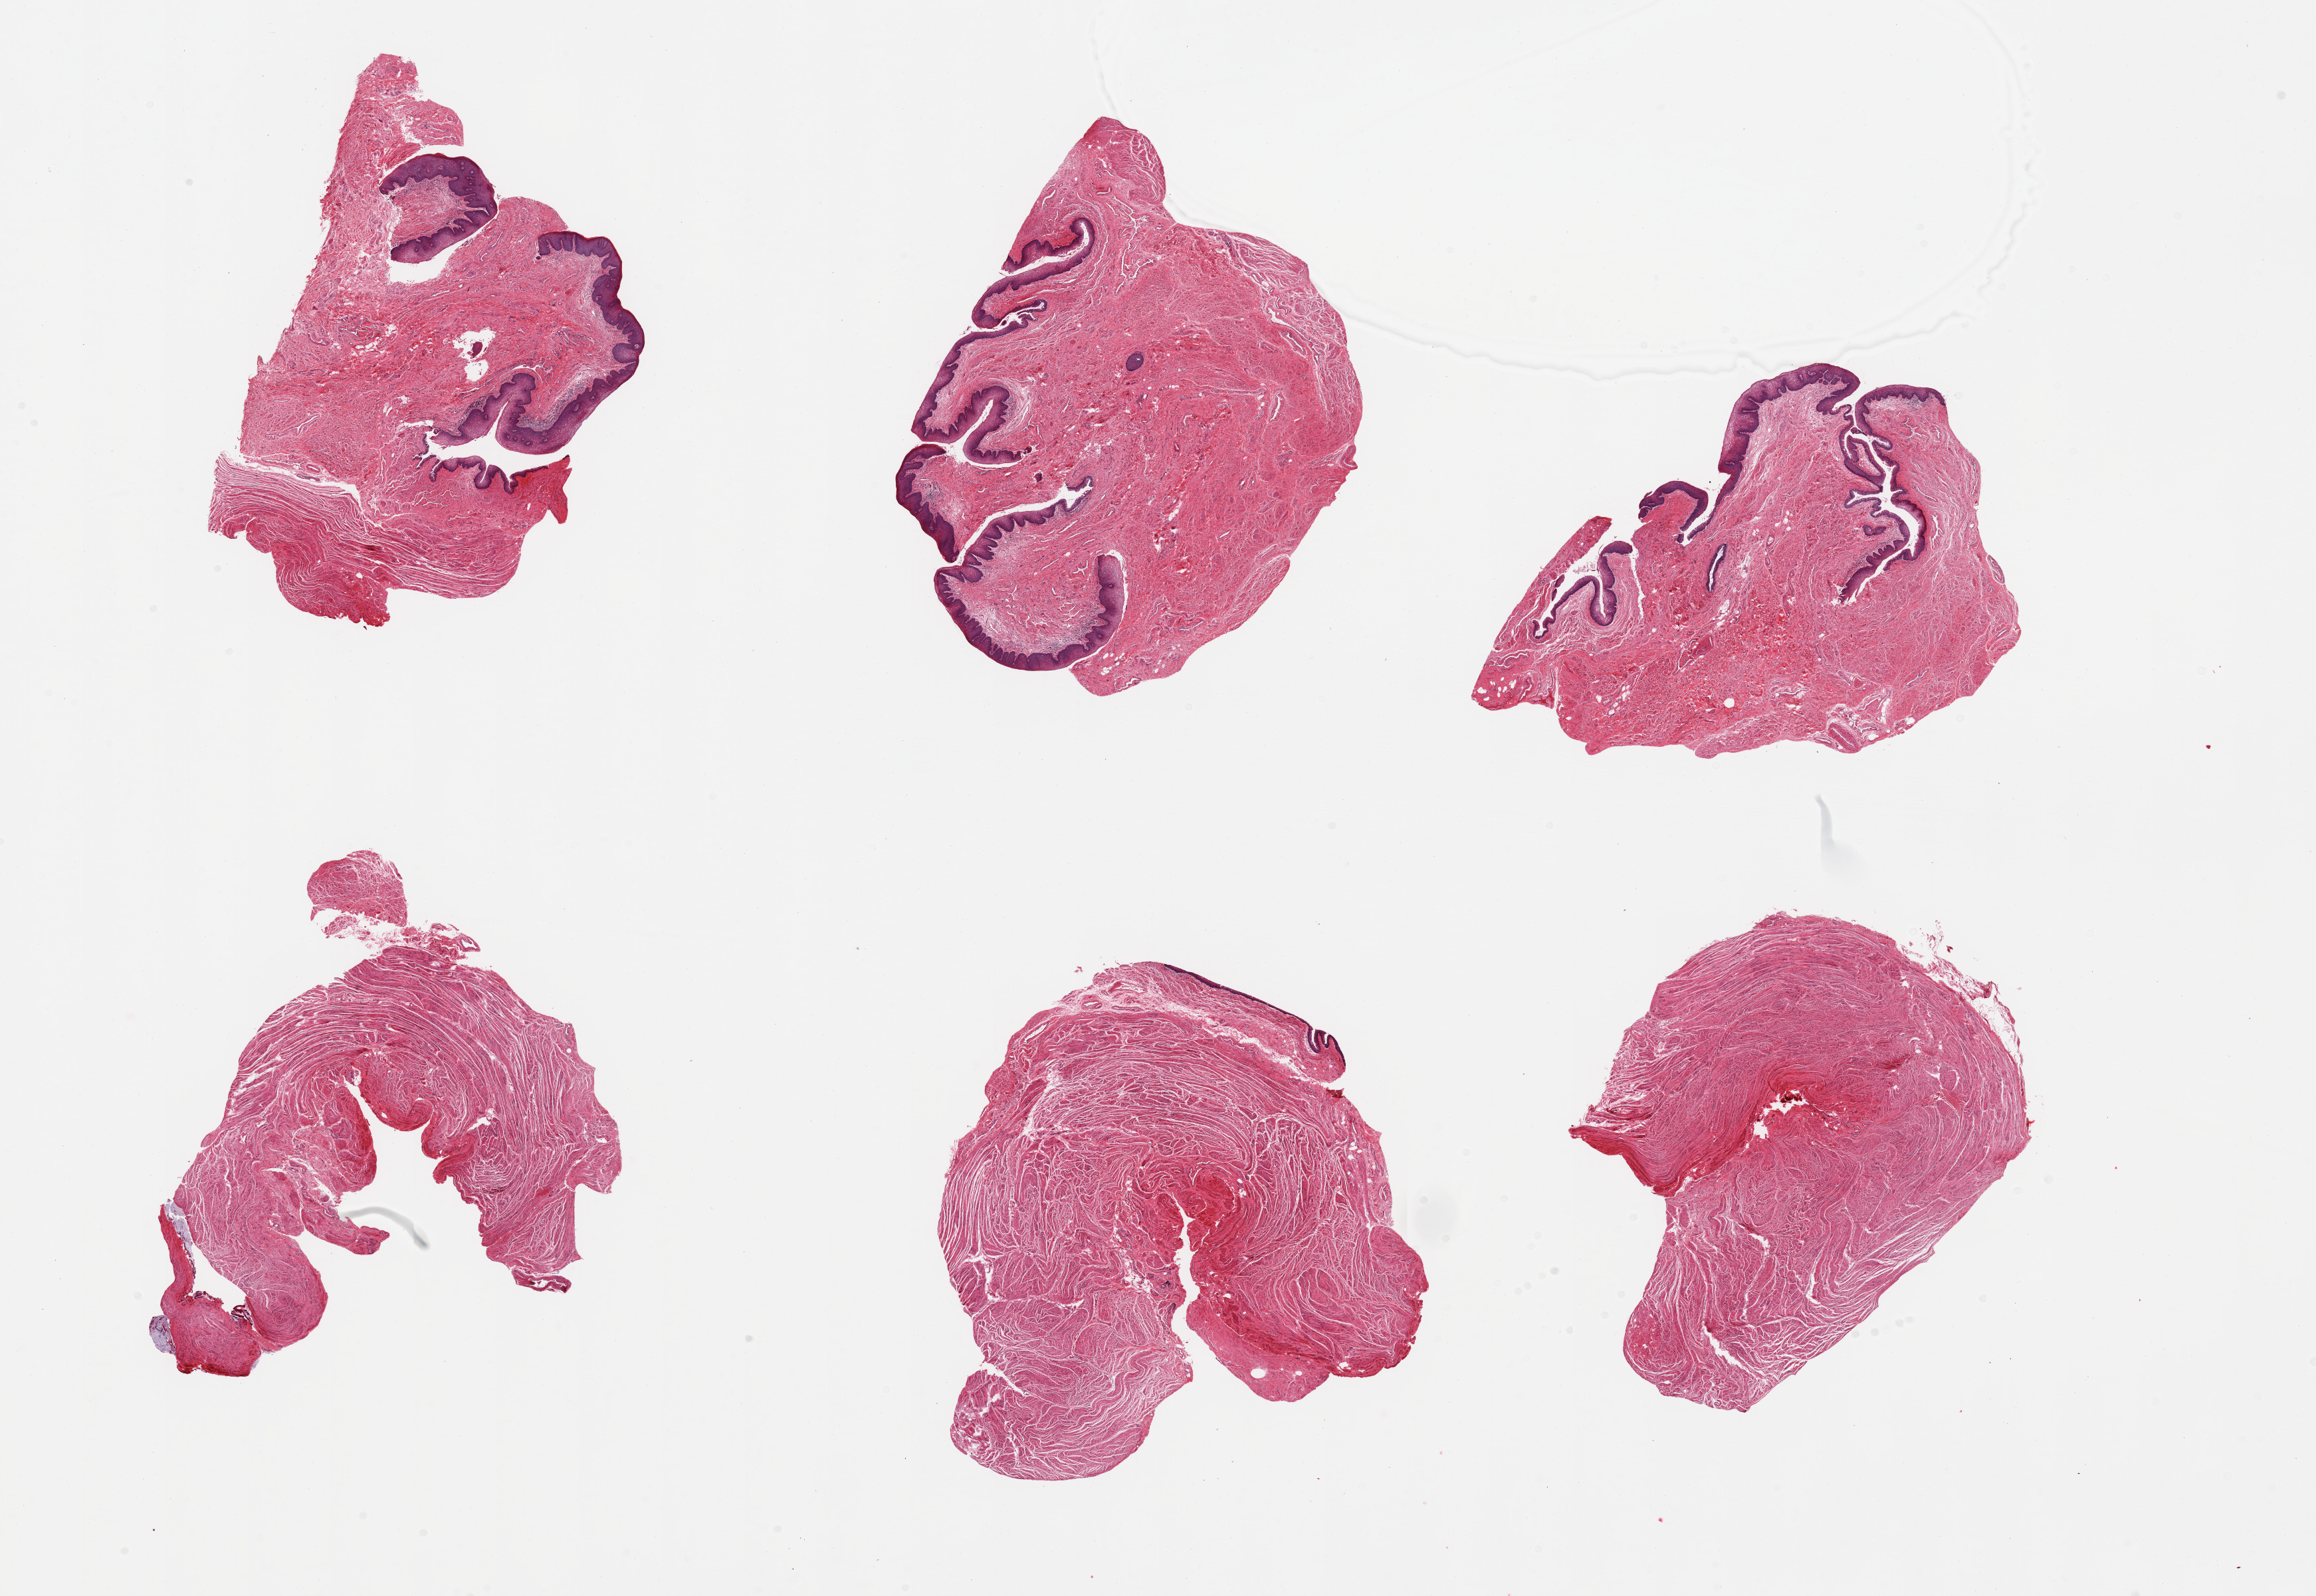
Whole-slide image, hematoxylin and eosin (H&E) stain — shown as a low-resolution overview of the whole scanned area (about 27.6 x 19.0 mm, acquisition: 20x scan), PAXgene-fixed paraffin-embedded (PFPE) section, section of vagina (target tissue), tissue donor sample. Female donor.
Reviewer comment on this tissue sample: 6 pieces, squamous mucosa ~0.3mm.